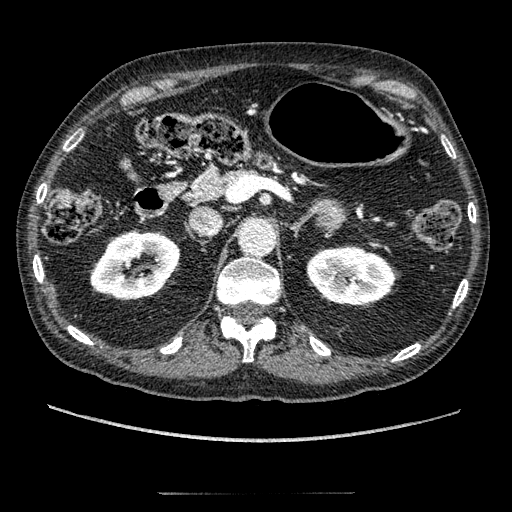
Contrast-enhanced abdominal CT, one axial slice; slice 125 of 274 in the series (ordered by position); reconstruction kernel STANDARD; 120 kVp; intravenous contrast given; soft-tissue window (W 400 / L 40 HU); 512 × 512 image matrix. Patient: male, 69 years. Case-level facts recorded for this patient, not image findings: diagnosis: adrenocortical carcinoma; tumour side: left adrenal; tumour size at pathology: 6.1 cm; Ki-67 index: 10 %; stage (as recorded): 3.
Structures marked on this image (semi-automatic segmentation, software-assisted and operator-edited):
- mass: box from (x=317, y=201) to (x=346, y=229) px